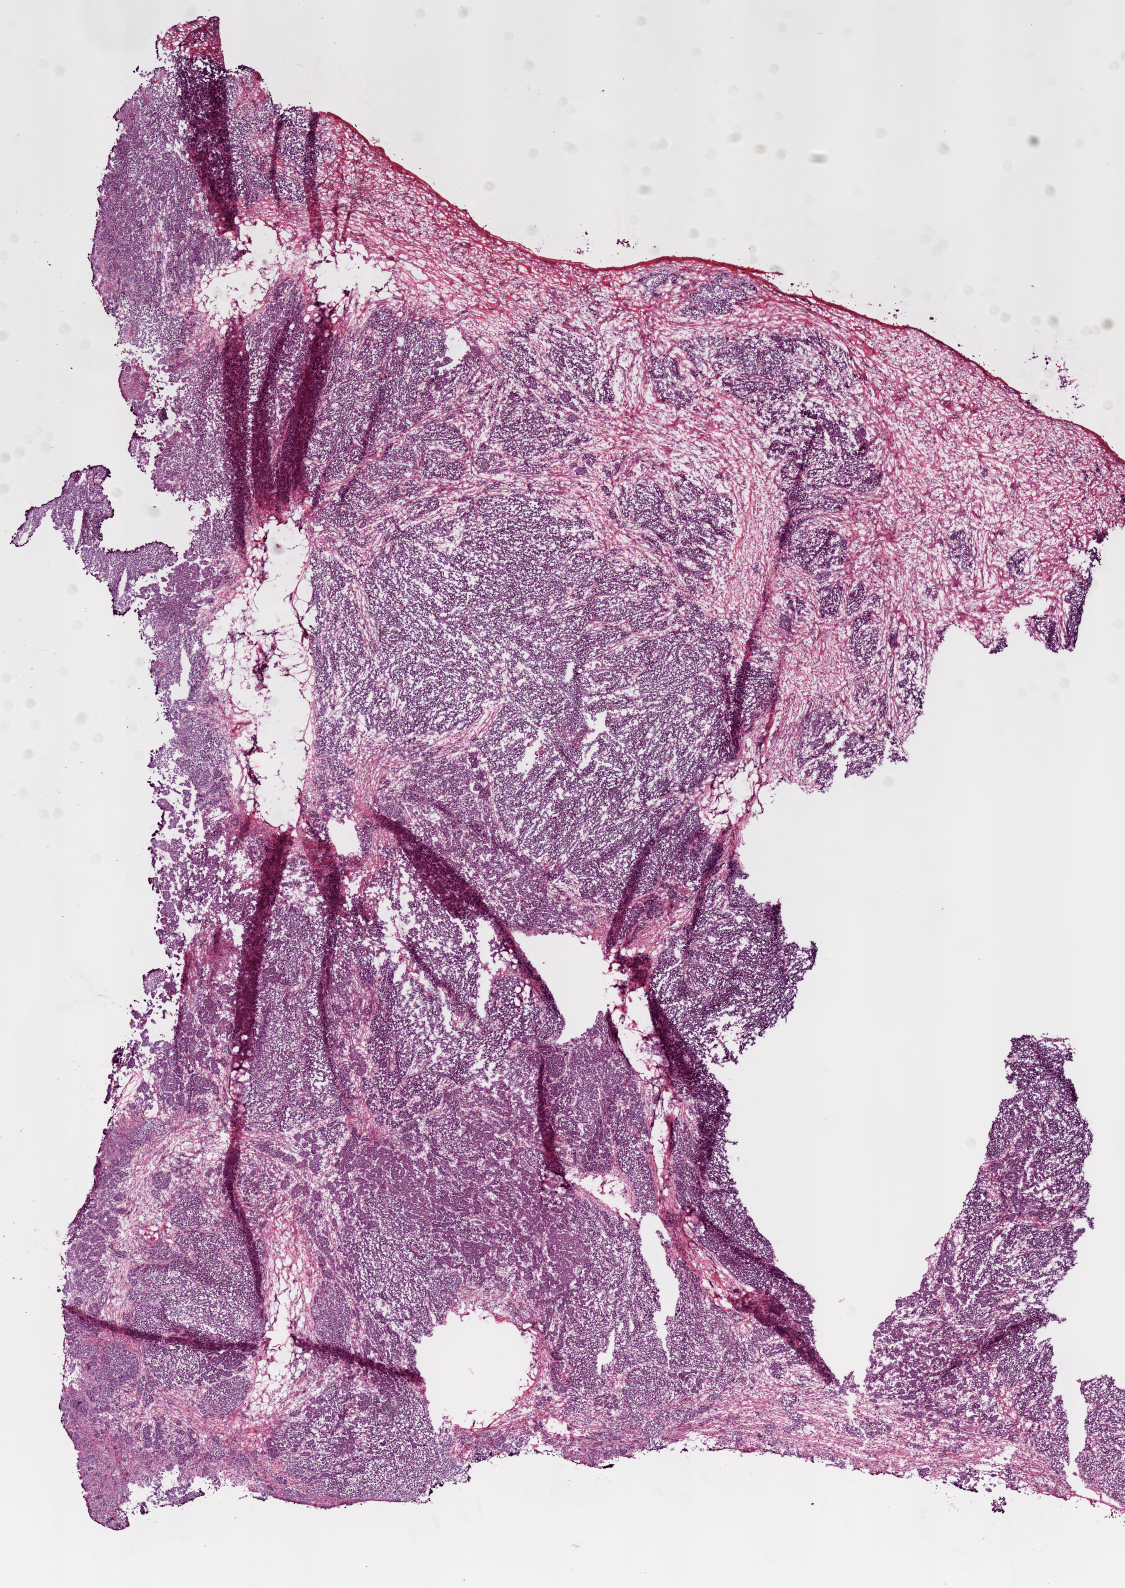
Digitized Hematoxylin and eosin (H&E) stained tissue section (whole slide) — shown as a low-resolution overview of the whole scanned area (about 9.0 x 12.7 mm). Frozen section. Primary tumour sample from the ovary. Patient: female, age at initial diagnosis 56 years. Pathologist review of this section (percent, as recorded): tumour cells 98%, tumour nuclei 90%.
Diagnosis: Serous cystadenocarcinoma, NOS.